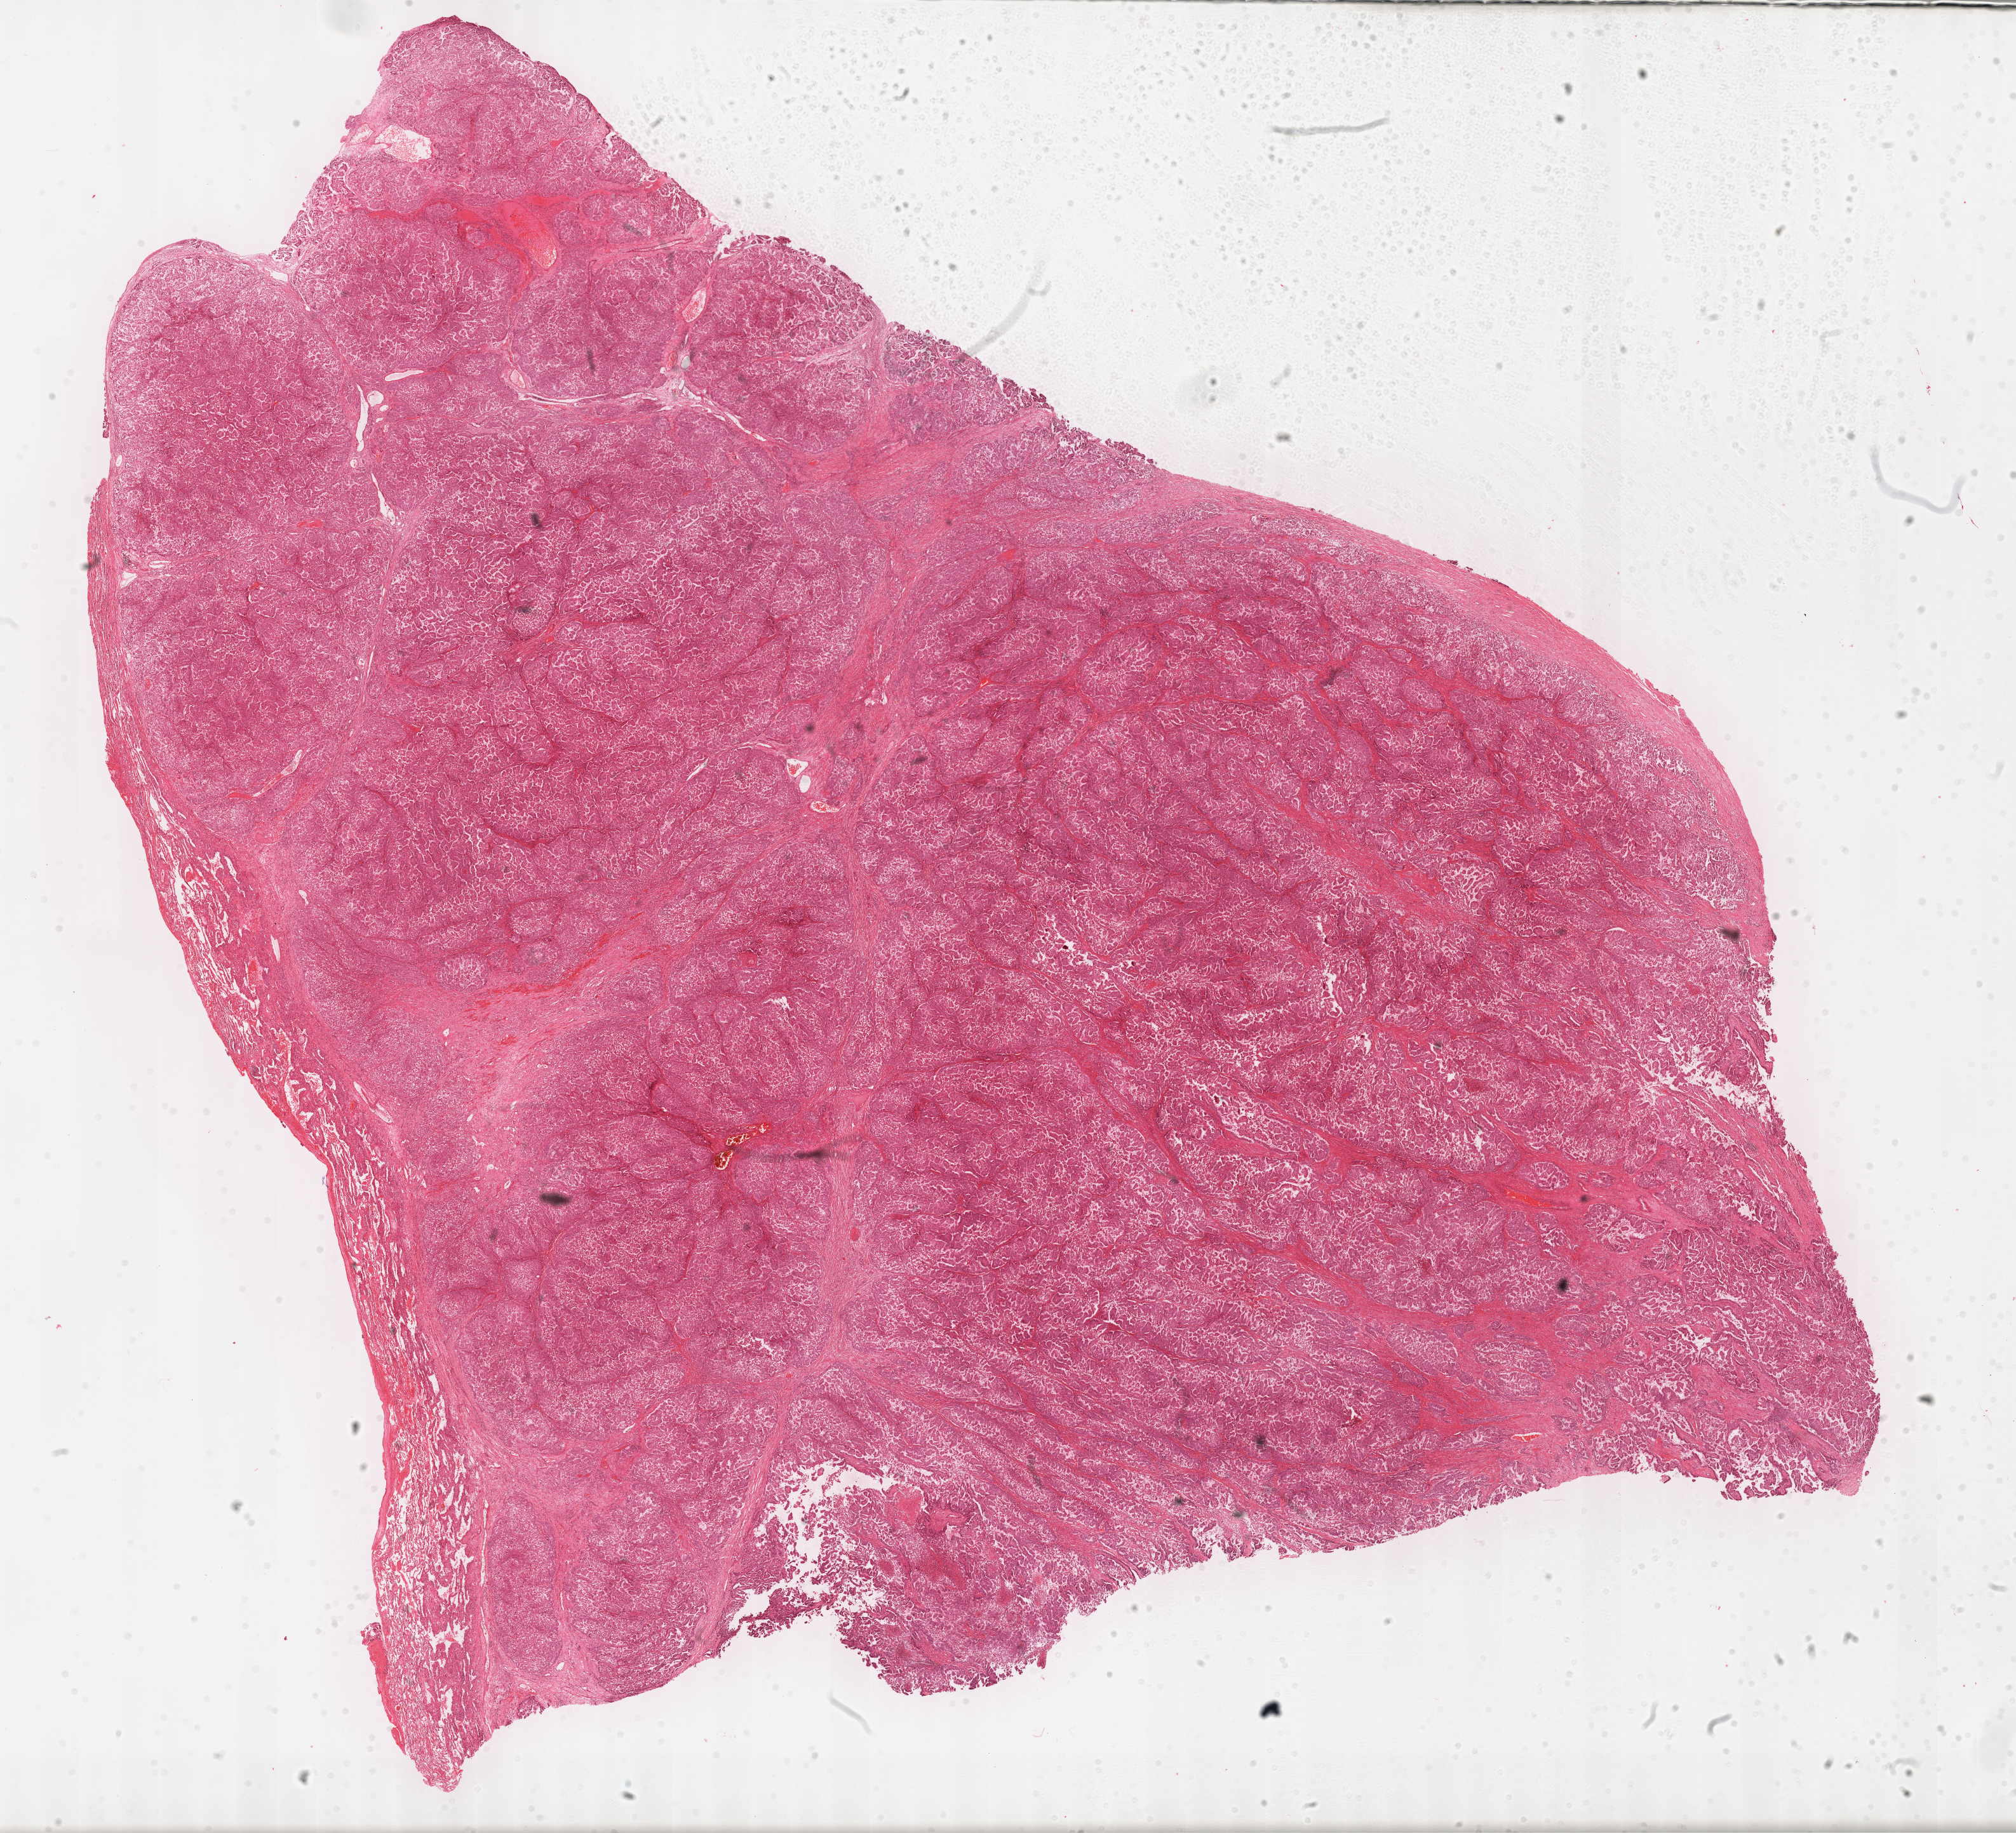
Digitized H&E tissue section (whole slide), a low-resolution overview of the entire scanned area, about 25.7 x 23.3 mm (slide scanned at 40x). FFPE section. Sample: primary tumour, mesothelium. Male patient; age at initial diagnosis 67 years.
Histologic diagnosis: Epithelioid mesothelioma, malignant (pleura, NOS).